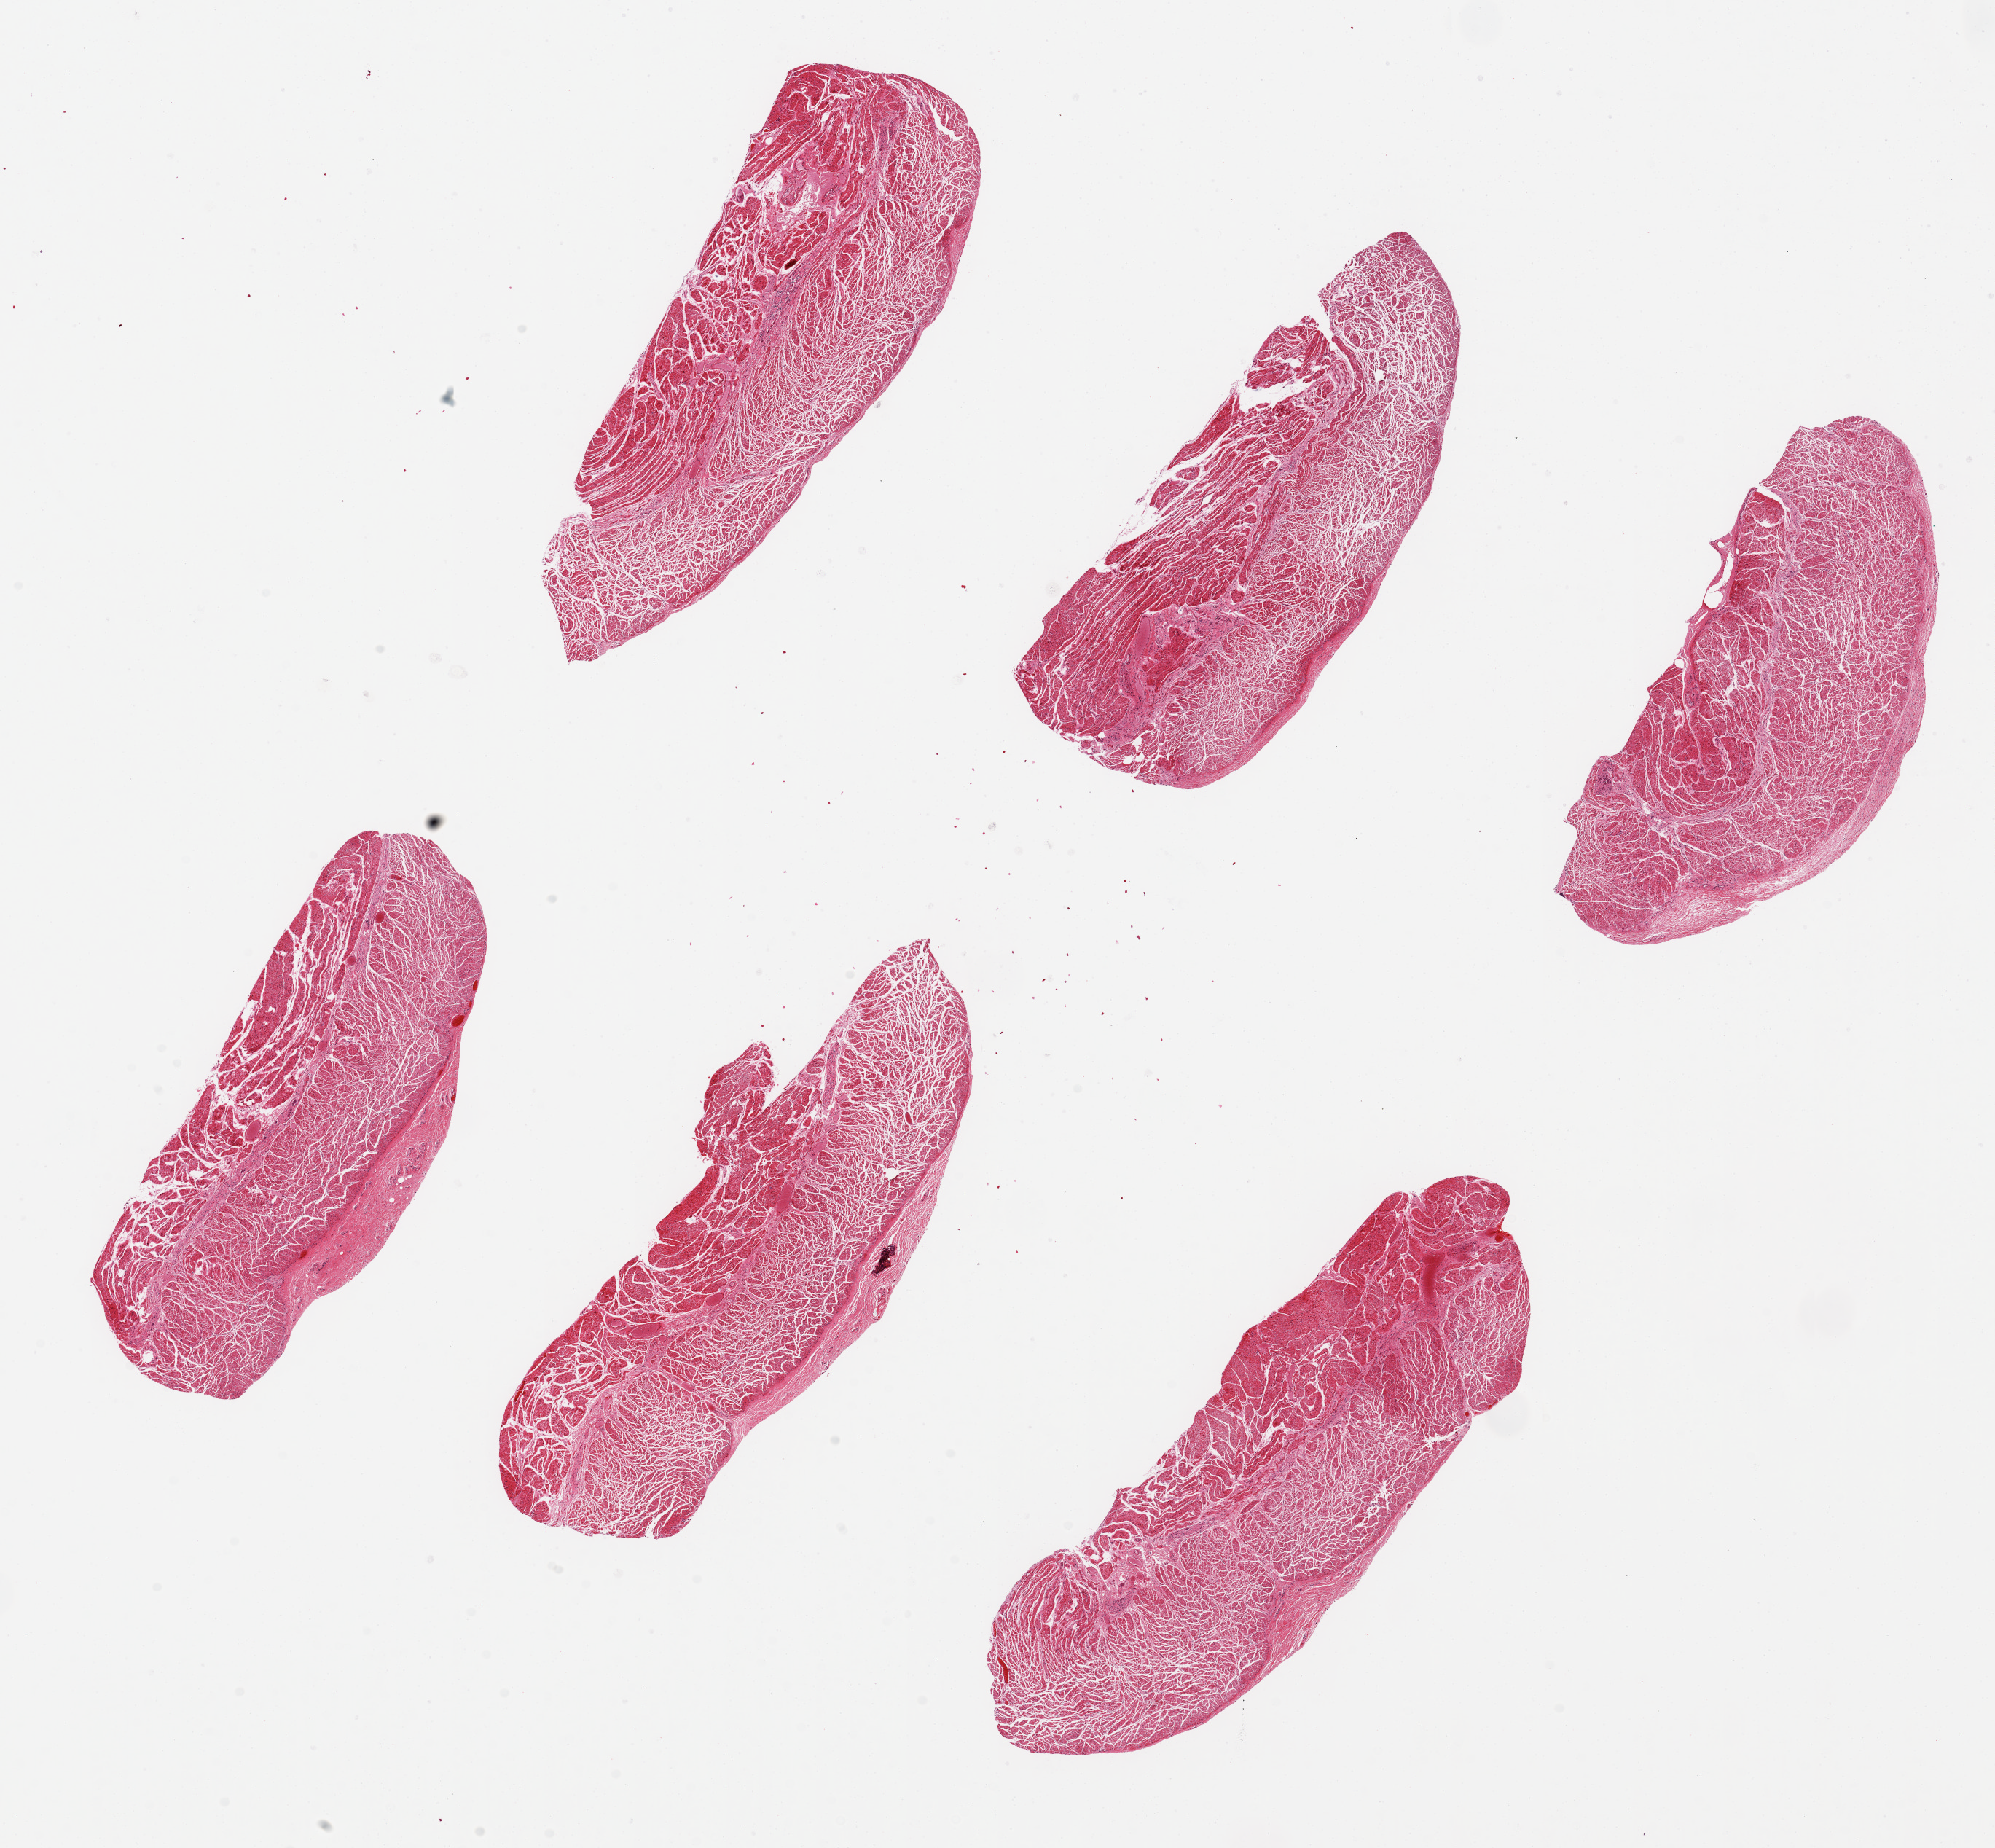
Whole-slide image, H&E stain, brightfield, shown as a low-resolution overview of the whole scanned area (about 21.7 x 20.1 mm). PAXgene-fixed, paraffin-embedded tissue. Sampled site (target tissue): esophageal muscle. Donor tissue sample. Male donor.
- pathologist's review note for this sample: 6 pieces ~7x2.5mm